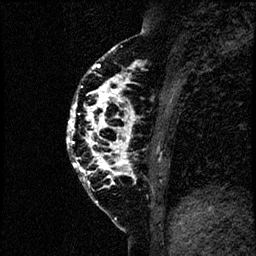
Breast MRI (dynamic contrast-enhanced), one sagittal slice. Slice 28 of 60 in the series (ordered by position). Dynamic contrast-enhanced study with each time point stored as its own series, time point 2 of 4 at this slice position (early post-contrast, ordered by acquisition time). 1.5 T. TE 4.2 ms, TR 17.6 ms. 2 mm slice thickness. 256 × 256 image matrix. Patient: female, 40 years. From the clinical record (not read from this slice): setting: breast cancer imaged before/during neoadjuvant chemotherapy; receptor status: HER2-positive.
Structures marked on this image (semi-automatic segmentation, software-assisted and operator-edited):
- analysis volume of interest (the breast-tissue region the enhancement analysis was run in; not a lesion): bounding box (x1, y1, x2, y2) in pixels: (66, 55, 184, 206)
- tumour enhancement mask (voxels above the 100 % enhancement threshold inside the analysis volume of interest): (66, 63, 137, 188)